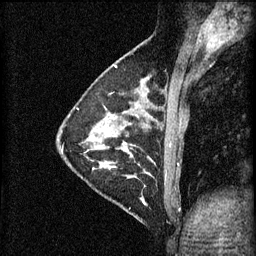
Breast MRI (dynamic contrast-enhanced), one sagittal slice. Position 21 of 60 along the scan axis. 3 images stored at this slice position (order not interpretable as contrast timing). 1.5 T. TE 4.2 ms, TR 11 ms. 2 mm slice thickness. 256 × 256 image matrix, field of view 180 × 180 mm. Female patient, age 29 years.
Structures marked on this image (semi-automatically segmented with operator editing):
- analysis volume of interest (the breast-tissue region the enhancement analysis was run in; not a lesion): box from (x=105, y=172) to (x=171, y=227) px
- tumour enhancement mask (voxels above the 70 % enhancement threshold inside the analysis volume of interest): (x=128, y=172)–(x=151, y=205)